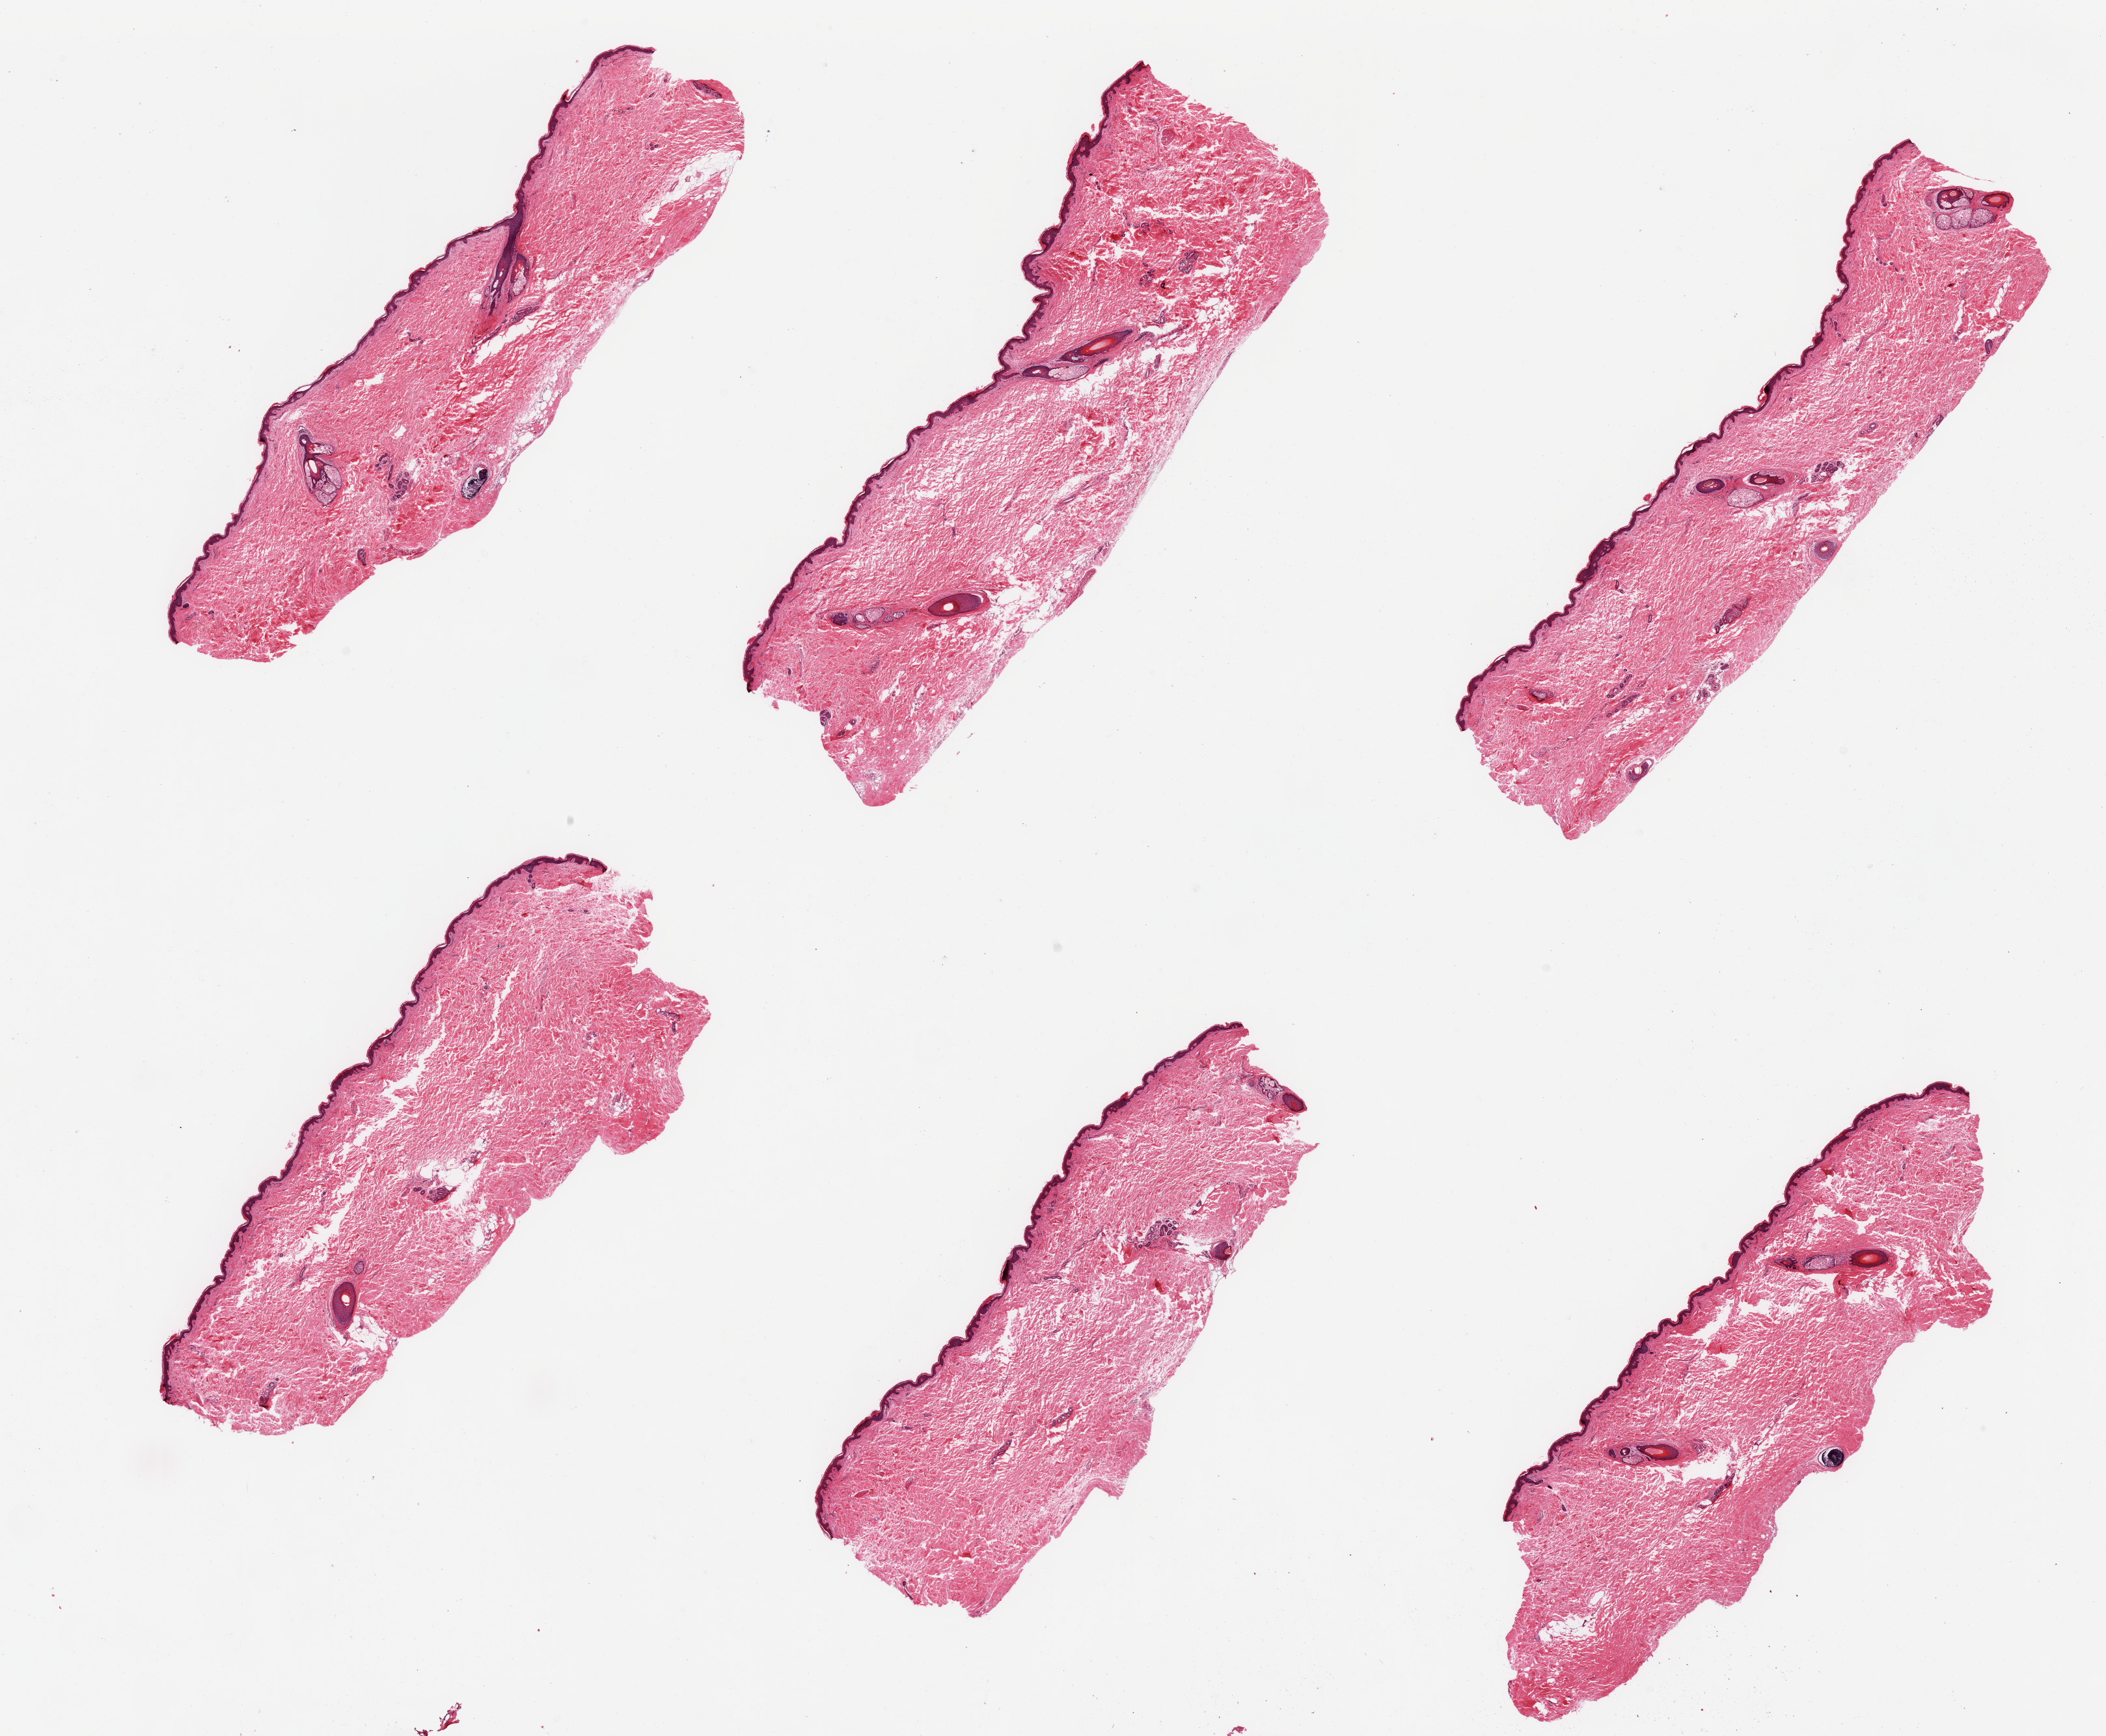
Hematoxylin and eosin (H&E) whole-slide image — a low-resolution overview of the entire scanned area, about 25.6 x 21.1 mm (from a 20x scan), PAXgene-fixed, paraffin-embedded tissue, target tissue: skin of suprapubic region, tissue donor sample. Donor sex: male.
Review note (as recorded): 6 pieces, minimal dermal fat ;squamous epithelium is ~50-60 microns.